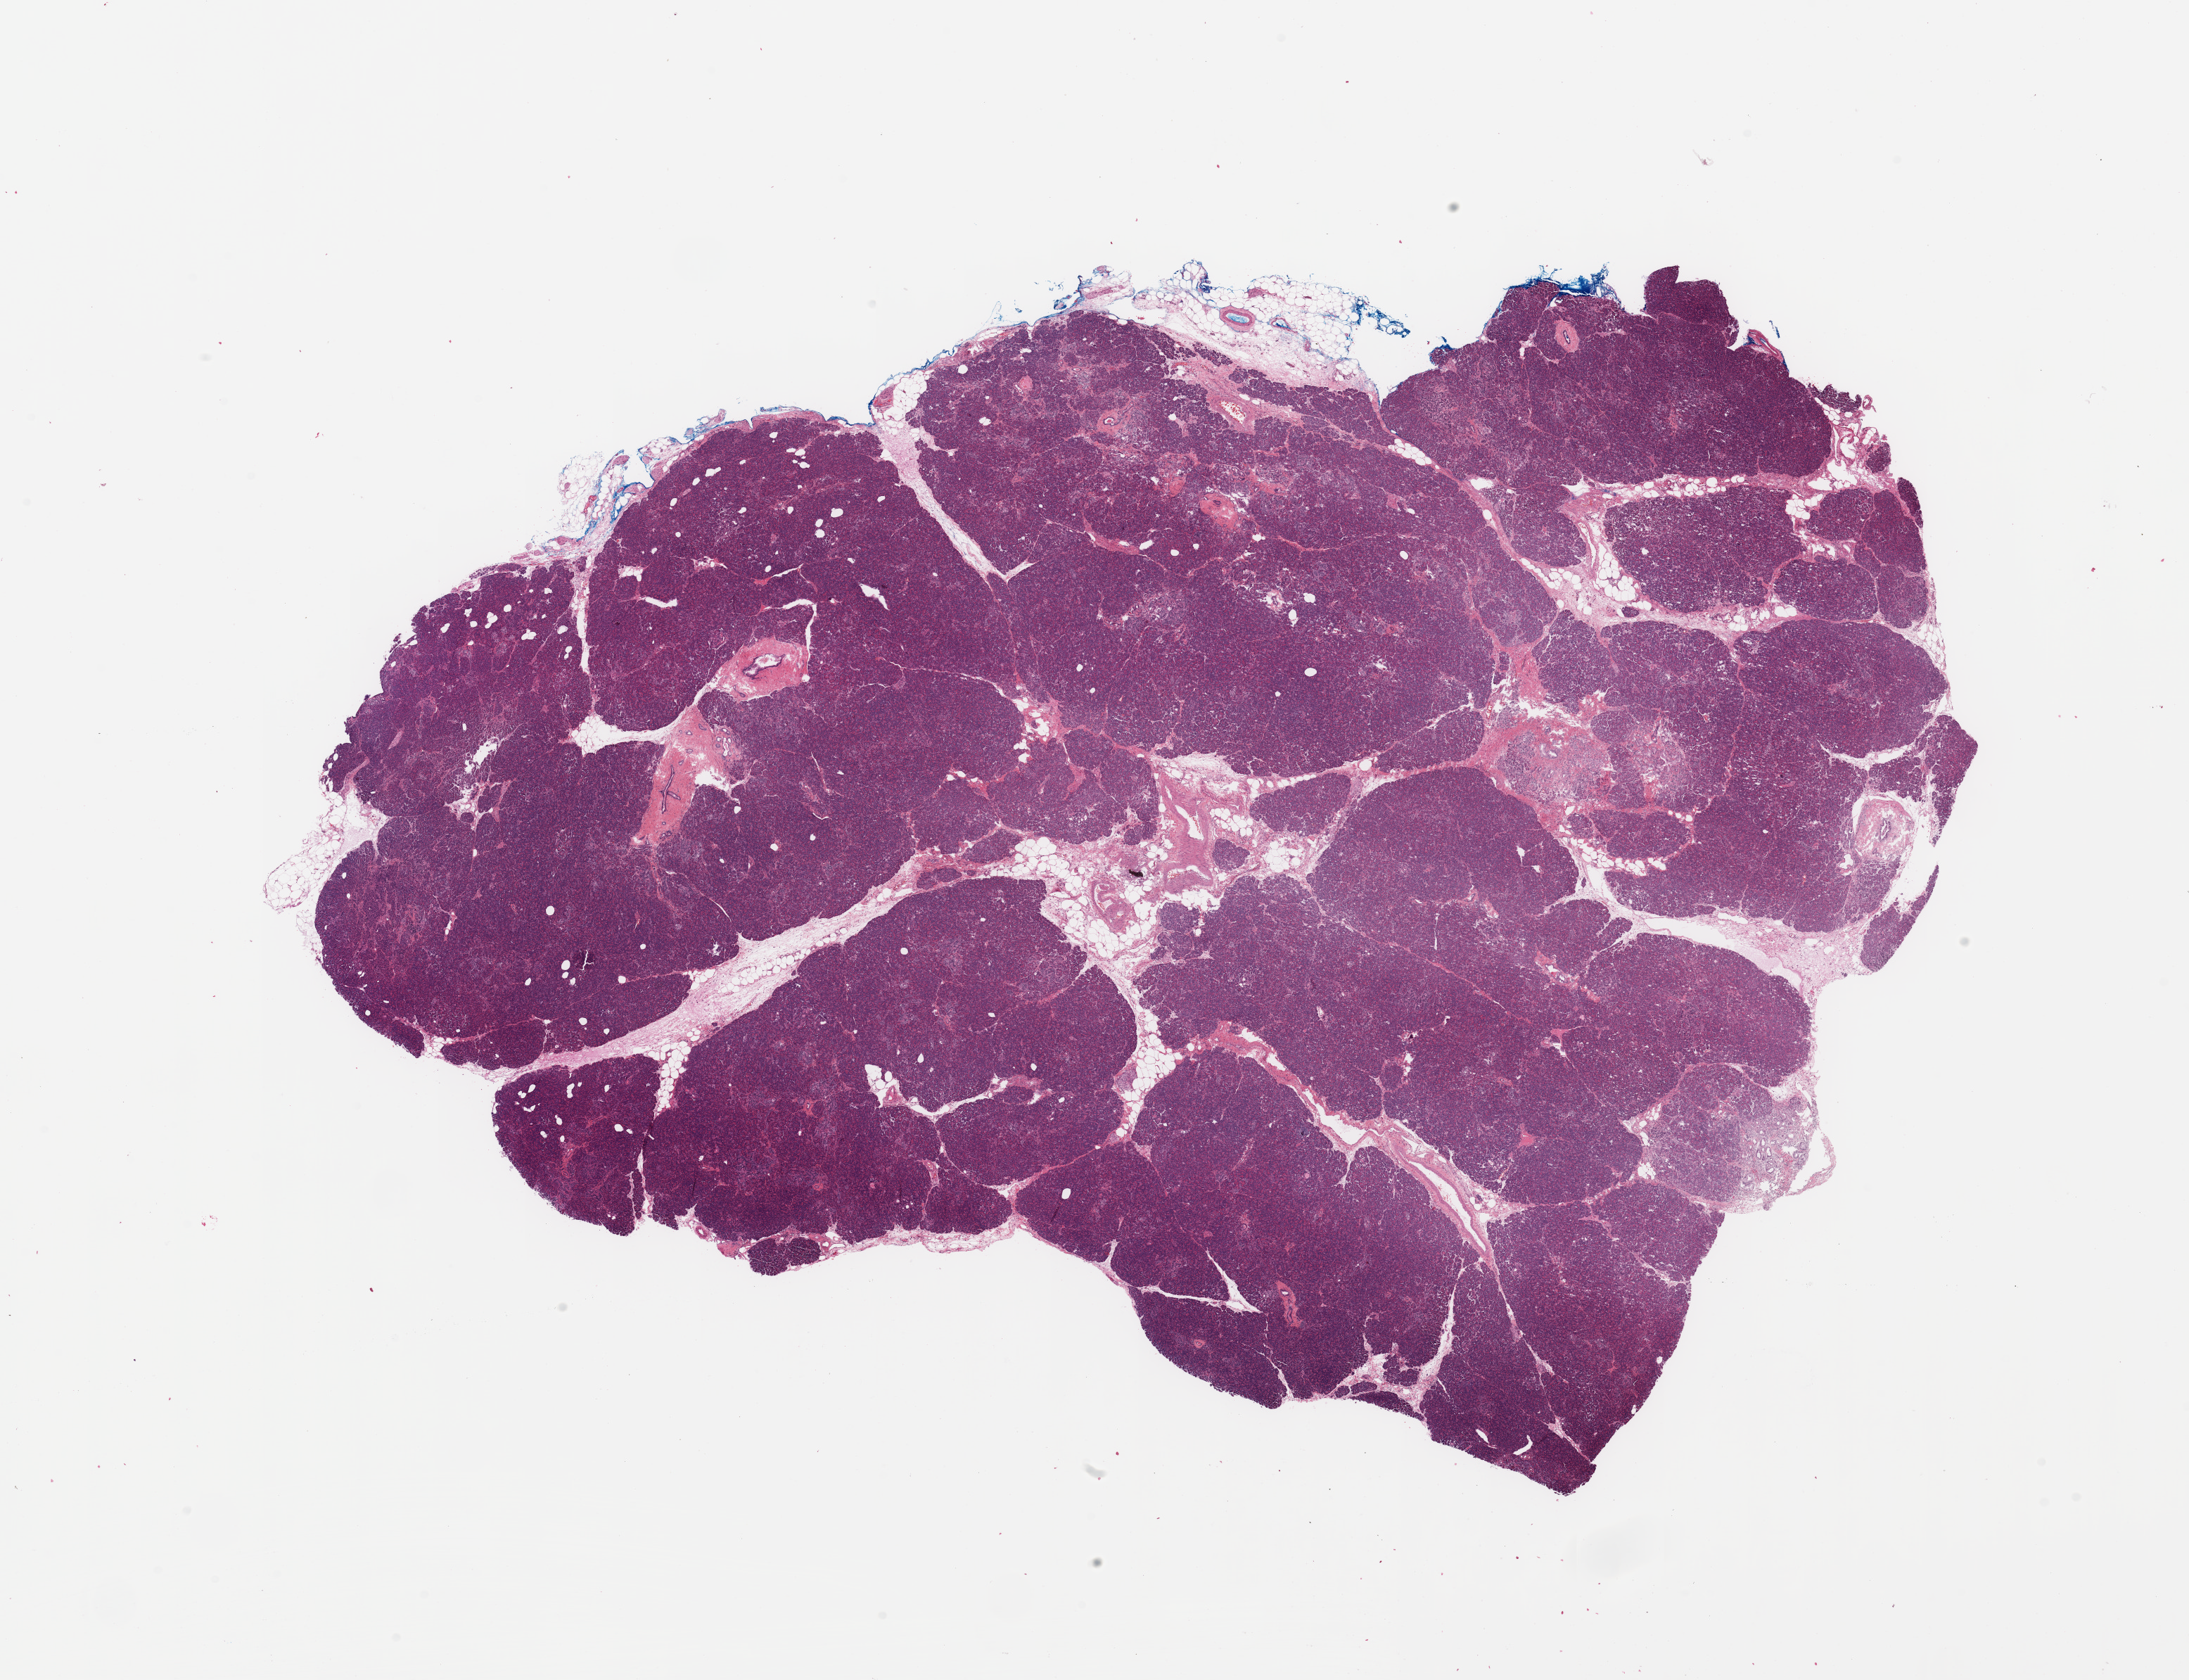
Digitized H&E tissue section (whole slide), low-resolution overview of the scanned area, about 24.6 x 18.9 mm (from a 20x scan), normal (non-tumour) tissue sample, sampled site: pancreas. Patient: female, age 64 years.
• this section: normal (non-tumour) tissue from the same patient
• patient diagnosis: Infiltrating duct carcinoma, NOS